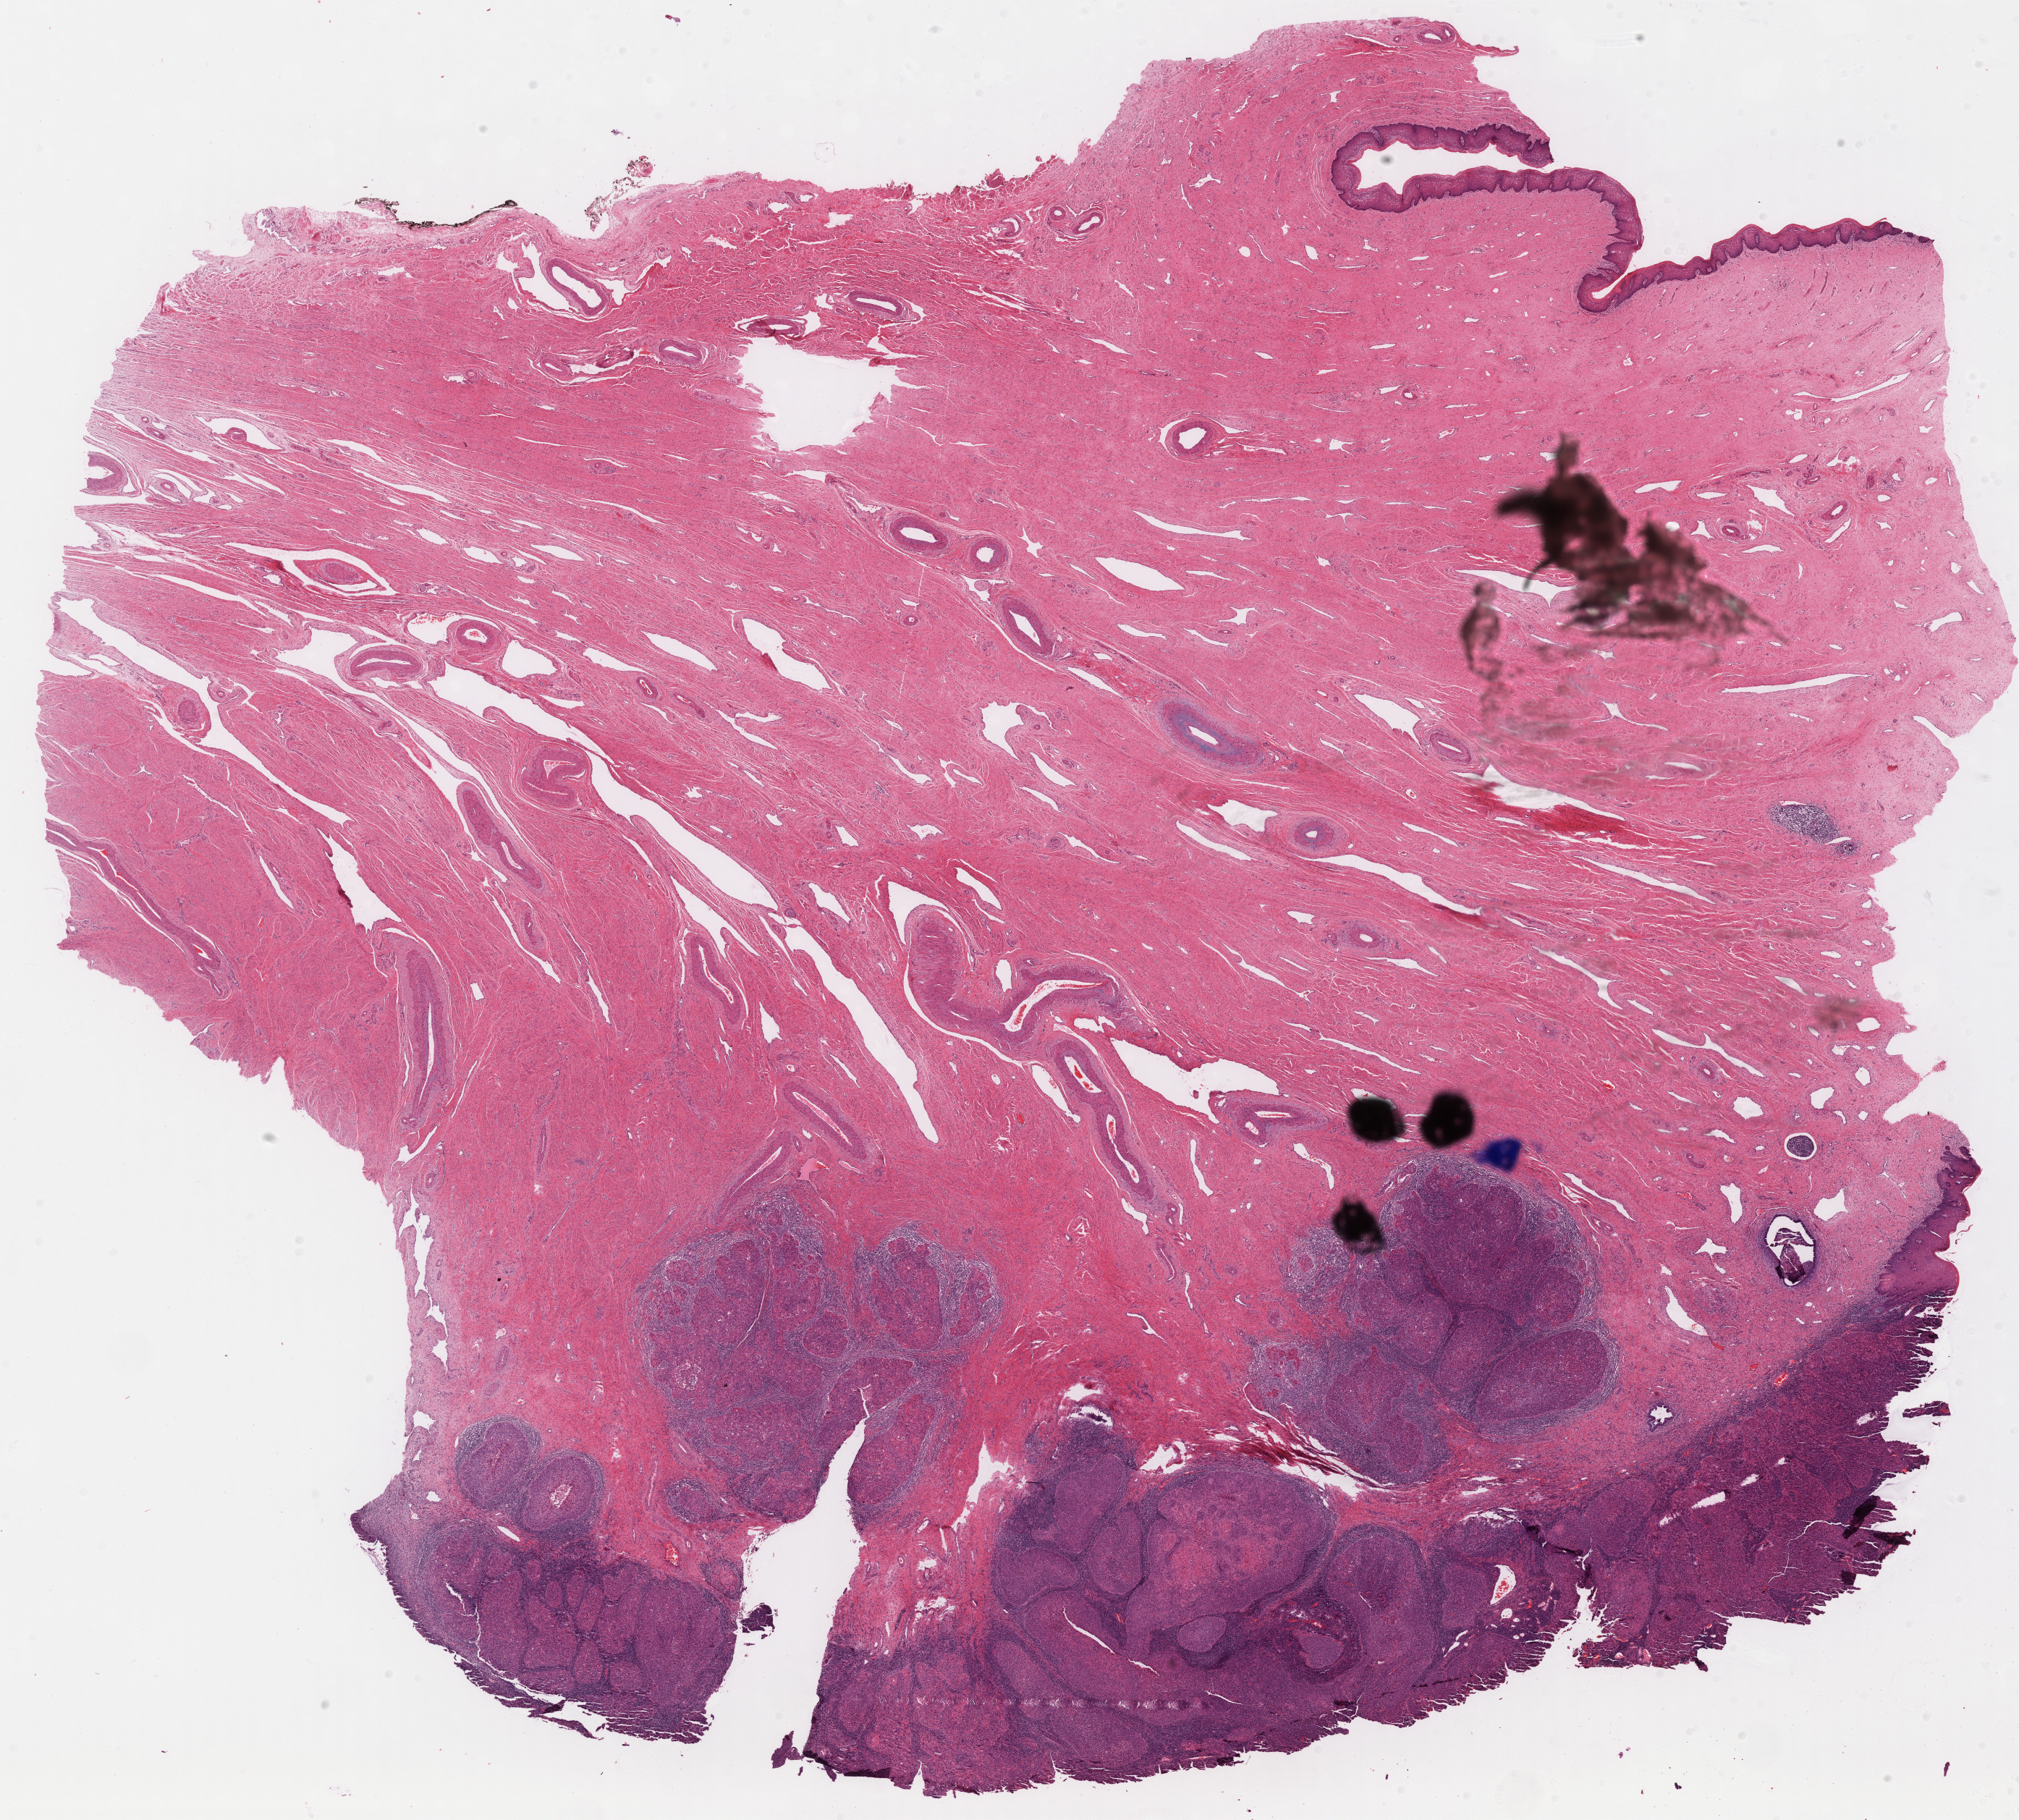
Digitized Hematoxylin and eosin (H&E) stained tissue section (whole slide) — a low-resolution overview of the entire scanned area, about 22.3 x 20.1 mm (acquisition: 40x scan); formalin-fixed paraffin-embedded (FFPE) diagnostic section; primary tumour sample from the cervix. Patient: female, age at initial diagnosis 36 years. Histologic grade: G2 (moderately differentiated).
• FIGO stage: IB
• pathologic diagnosis: Squamous cell carcinoma, NOS (cervix uteri)